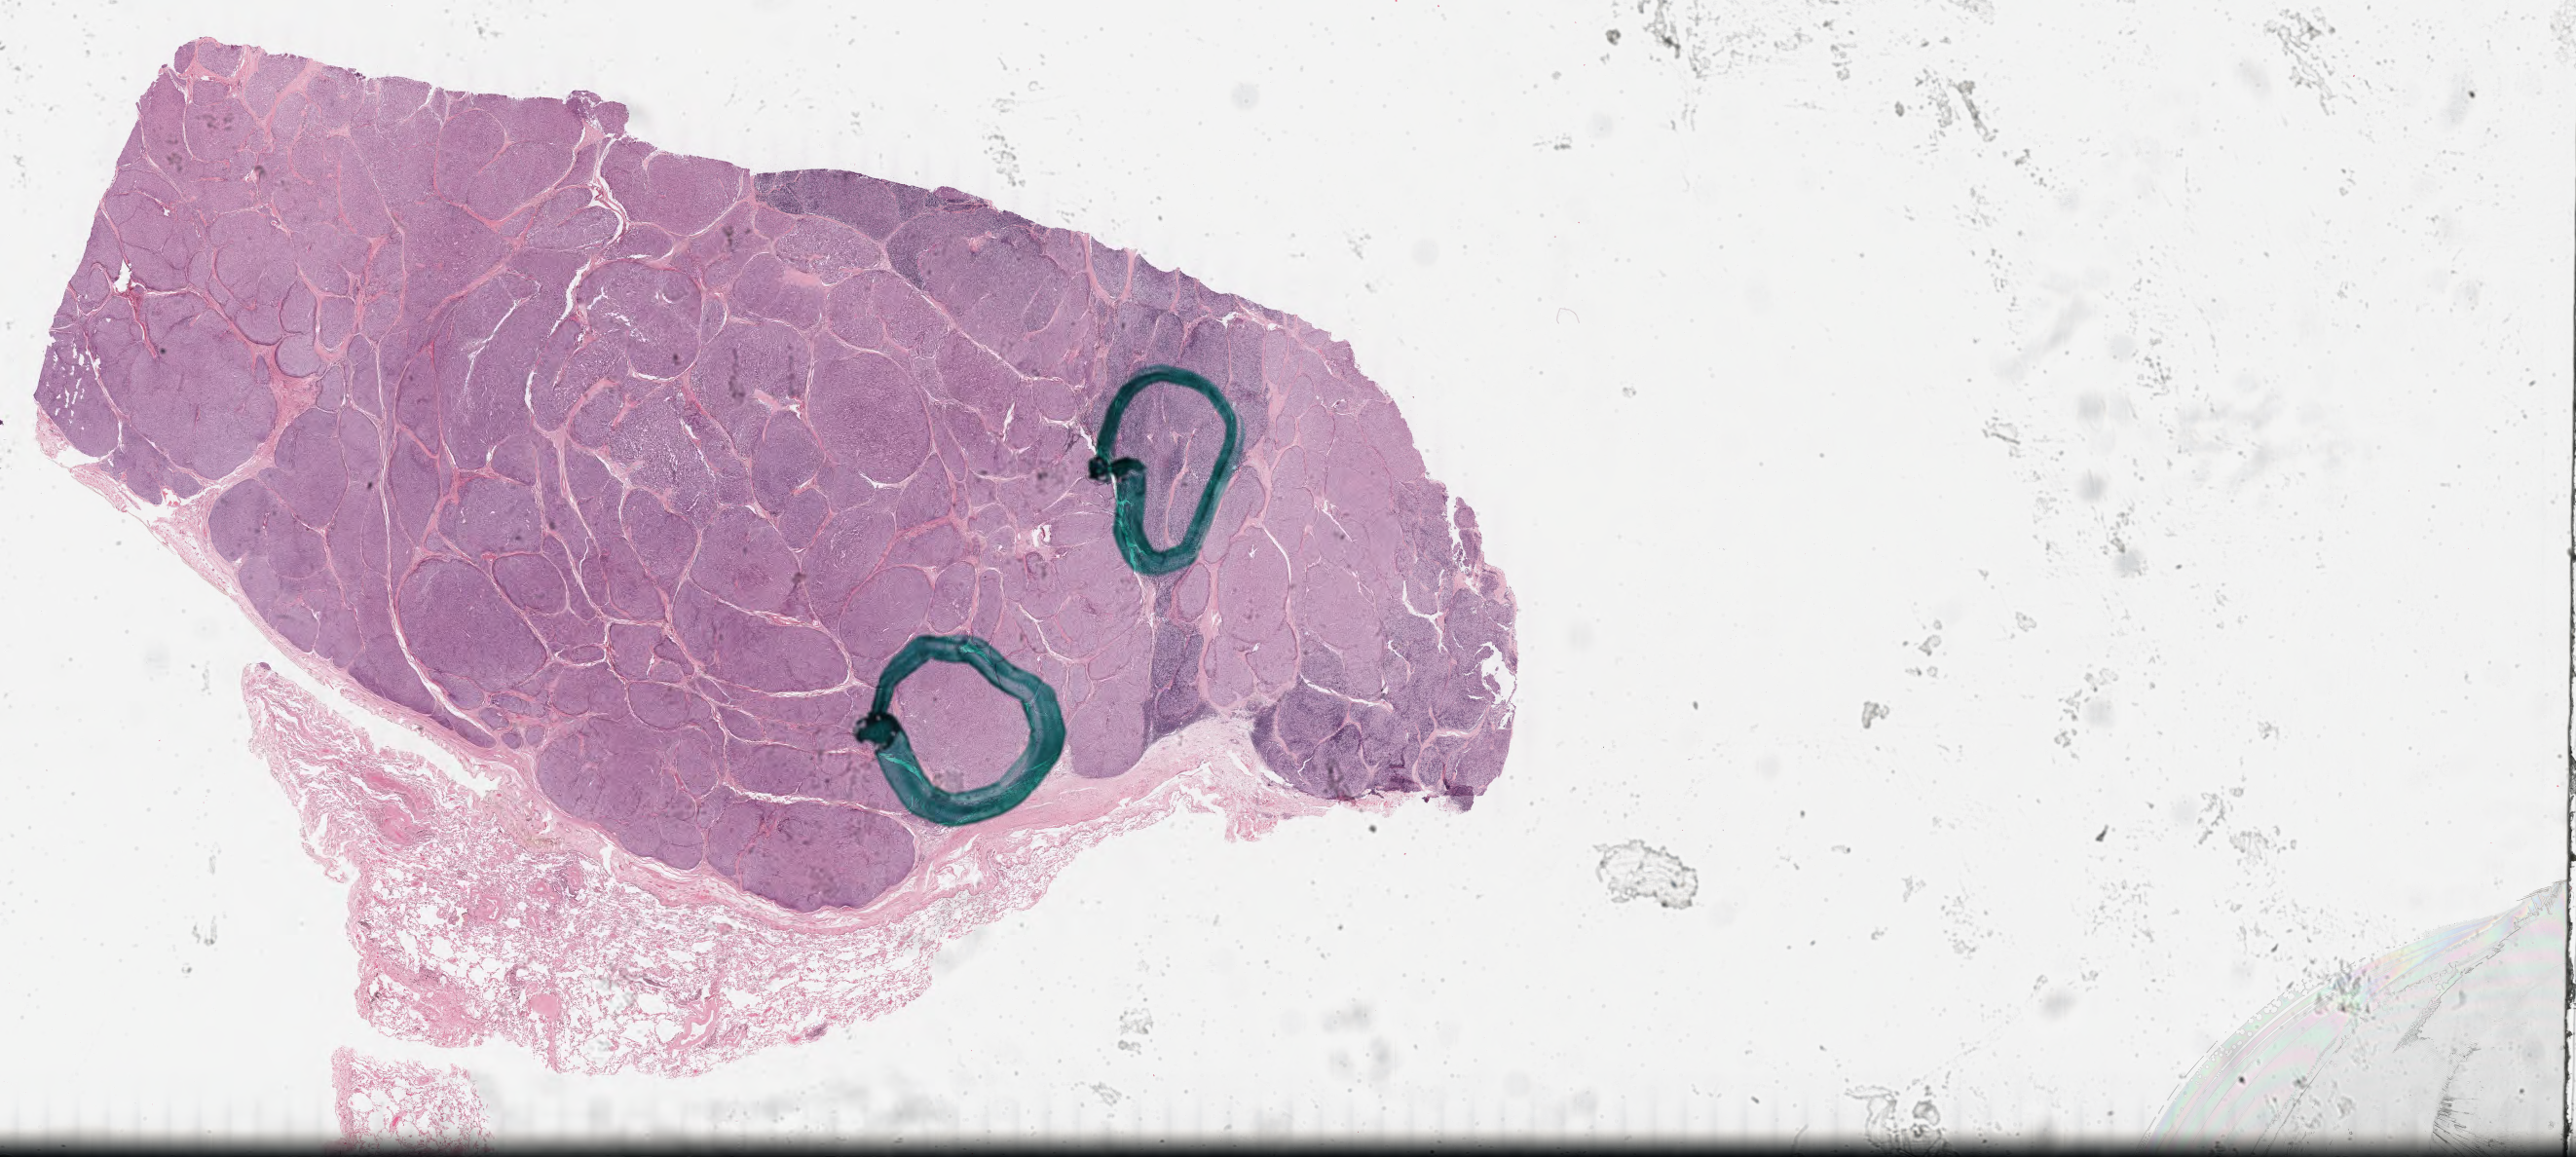
Hematoxylin and eosin (H&E) stained whole-slide image — shown as a low-resolution overview of the whole scanned area (about 41.8 x 18.8 mm, slide scanned at 40x). FFPE section. Thymus, primary tumour sample. Male patient; age at initial diagnosis 61 years.
- diagnosis: Thymoma, type AB, malignant